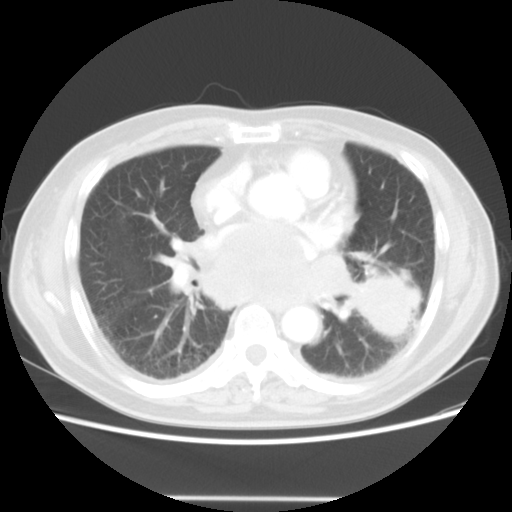
Chest CT, one axial slice; slice 24 of 56 in the series (ordered by position); reconstruction kernel STANDARD; lung window (W 1500 / L -600 HU); 5 mm slice thickness; 512 × 512 image matrix. Male patient, age 66 years. From the clinical record (not read from this slice): clinical TNM (as recorded): T4 N3 M0.
Outlined on this slice (rectangle marked by the reading radiologist):
- lung tumour (recorded histology: small cell carcinoma): box from (x=358, y=258) to (x=423, y=351) px